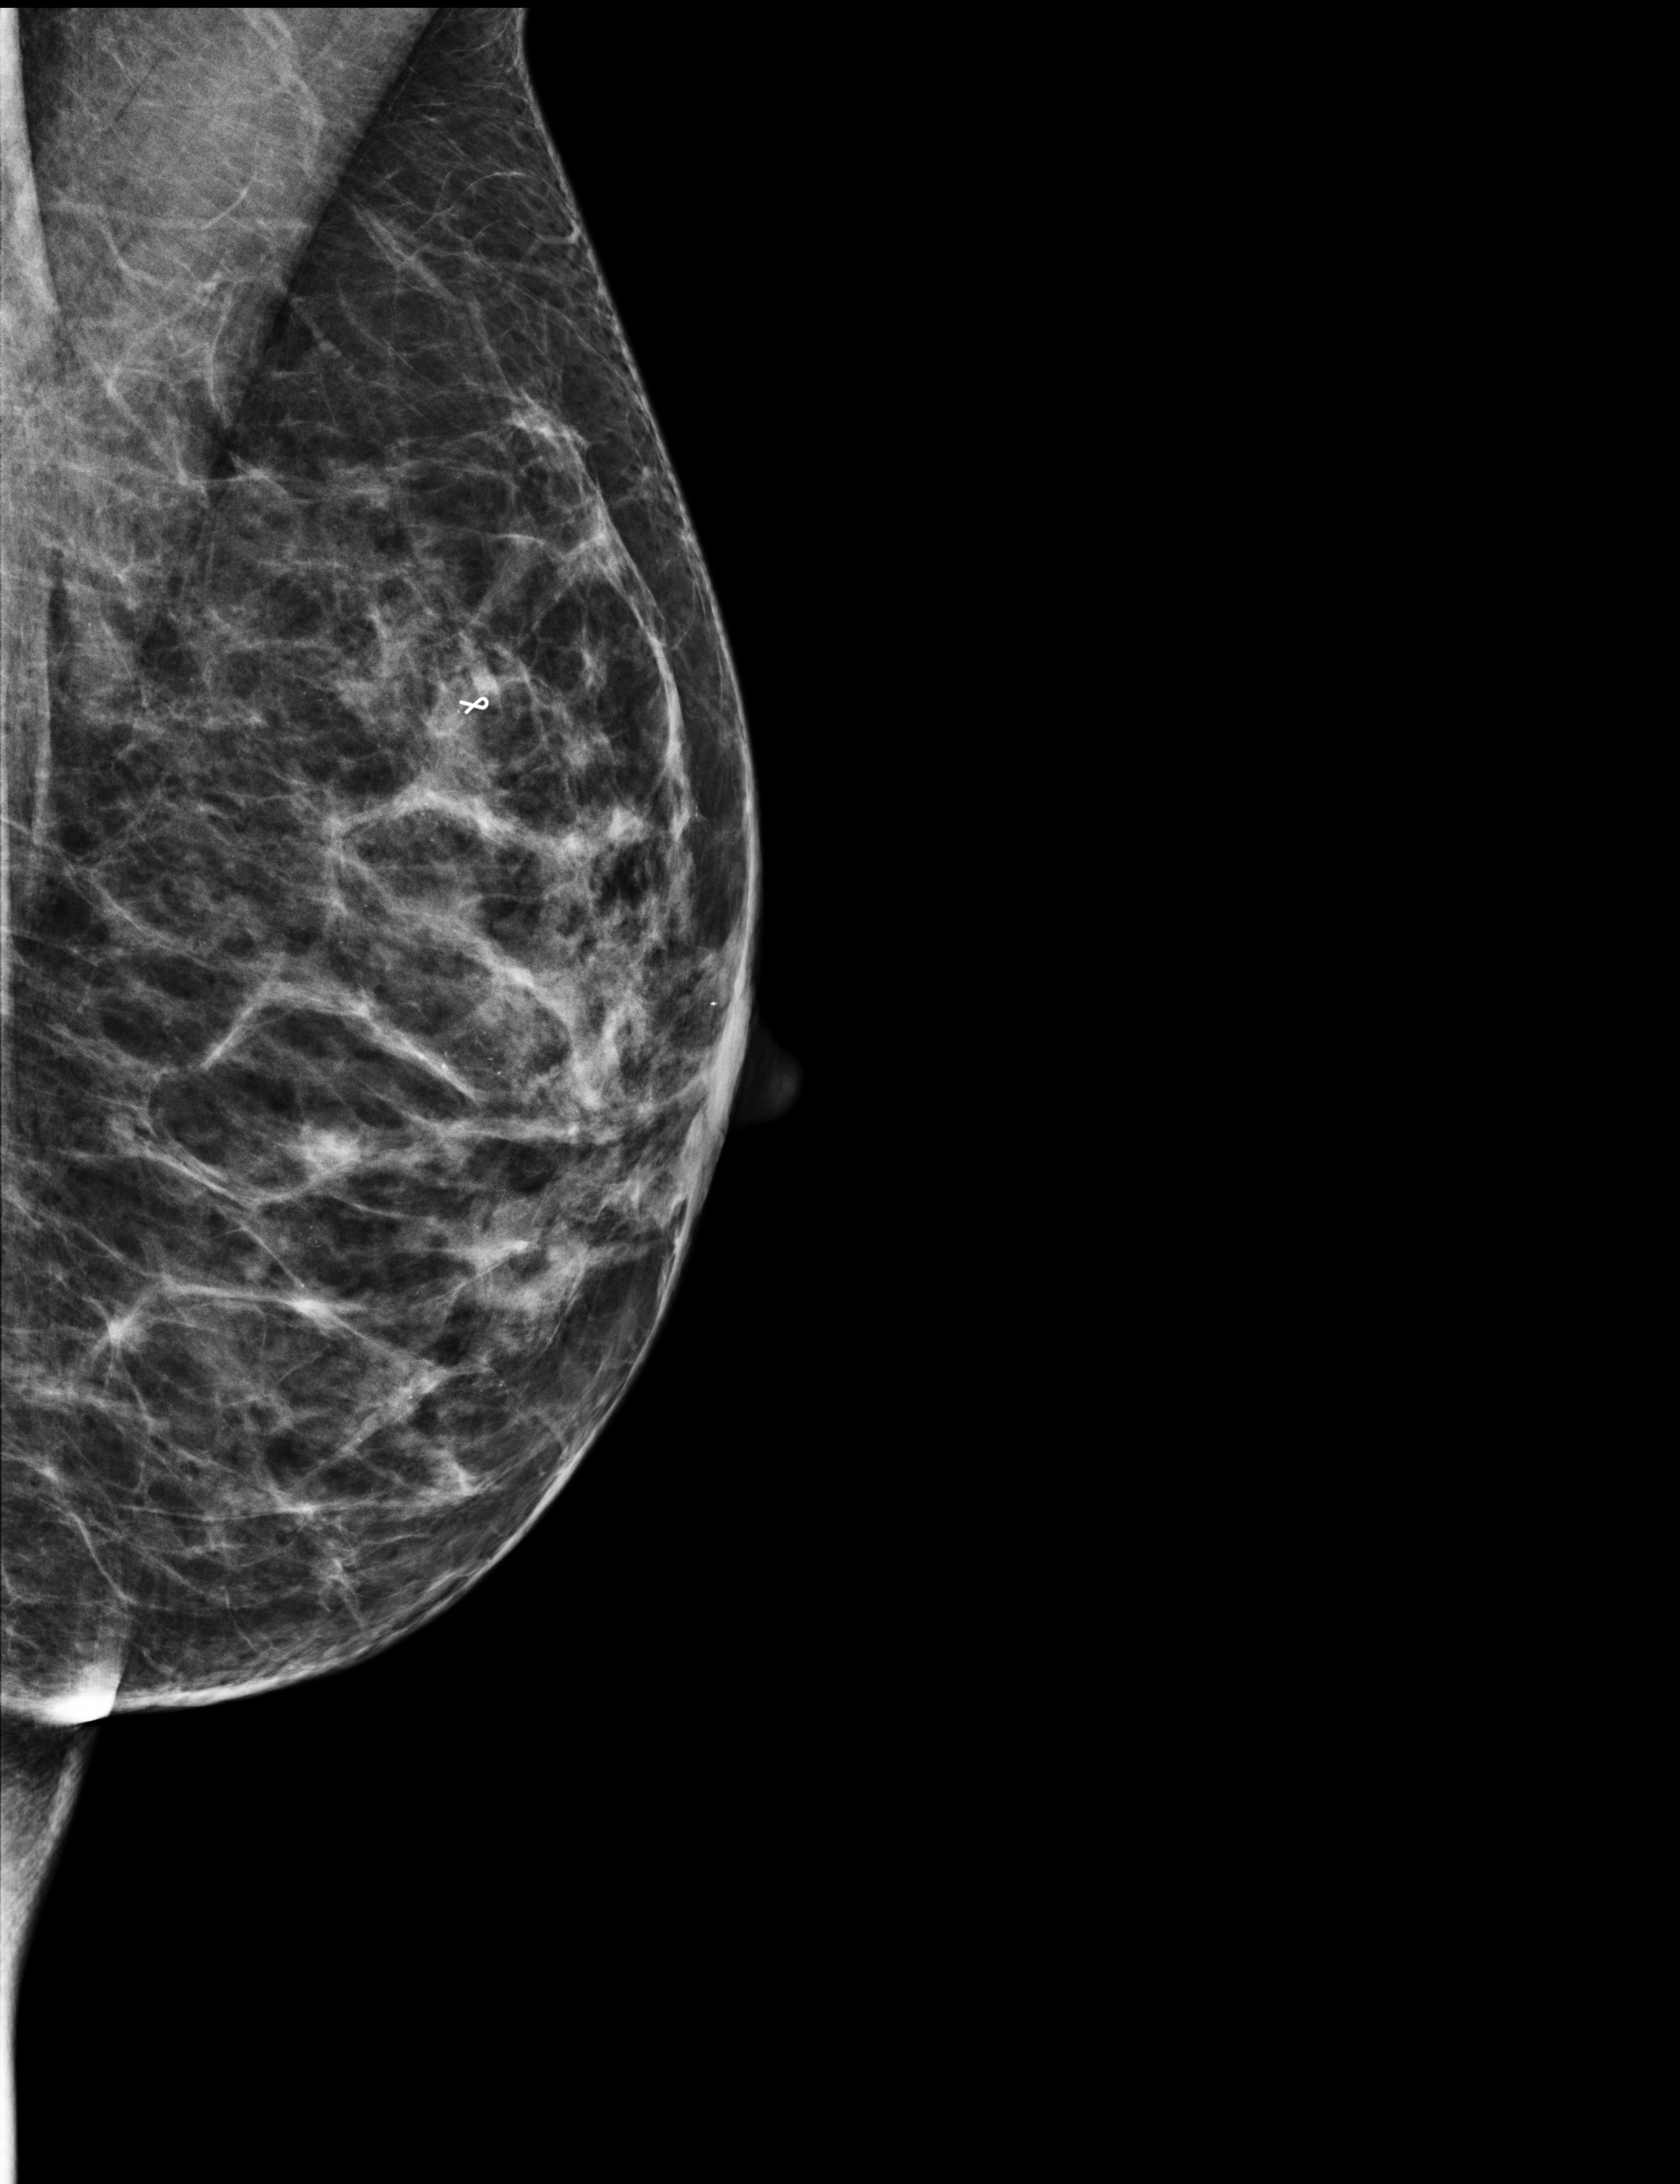
Diagnostic work-up study. Patient aged 51 years (female).
Image type: full-field digital mammogram. Breast: left. Projection: ML view.